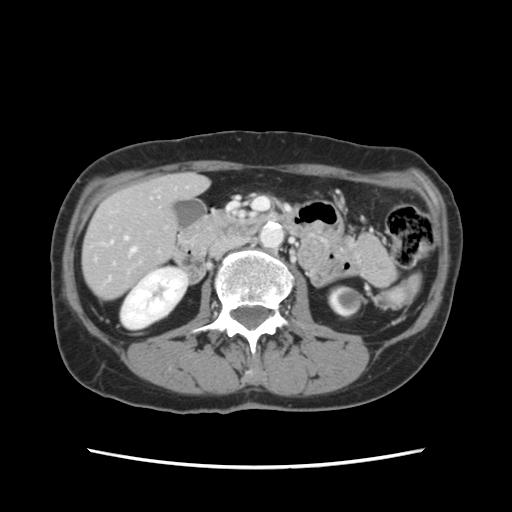
Contrast-enhanced abdominal CT, one axial slice; position 40 of 120 along the scan axis; intravenous contrast given; soft-tissue window (W 400 / L 40 HU); 2.5 mm slice thickness; 512 × 512 image matrix, field of view 330 × 330 mm. Female patient, age 70 years. Case-level facts recorded for this patient, not image findings: diagnosis: colorectal cancer liver metastases, imaged before liver resection; multiple liver metastases: no; largest metastasis: 2.5 cm.
Outlined on this slice (expert manual segmentation):
- hepatic veins: bounding box (x1, y1, x2, y2) in pixels: (131, 248, 136, 253)
- liver: (83, 175, 206, 298)
- planned liver remnant (the part of the liver to remain after resection): (83, 175, 206, 299)
- portal vein (with intrahepatic branches): (125, 236, 128, 240)